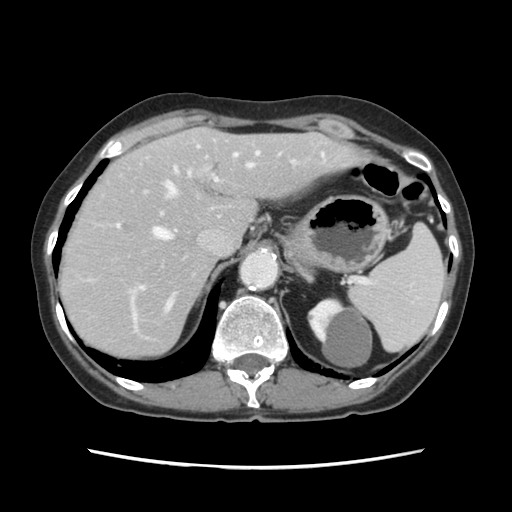
Contrast-enhanced abdominal CT, one axial slice; position 89 of 120 along the scan axis; intravenous contrast given; soft-tissue window (W 400 / L 40 HU); 512 × 512 image matrix, field of view 330 × 330 mm. Female patient, age 70 years. From the clinical record (not read from this slice): diagnosis: colorectal cancer liver metastases, imaged before liver resection; multiple liver metastases: no; largest metastasis: 2.5 cm; disease in both lobes: no.
Annotated regions visible in this slice (expert manual segmentation):
- hepatic veins: bounding box <153,153,253,313> (left, top, right, bottom; pixels)
- liver: <61,129,353,357>
- planned liver remnant (the part of the liver to remain after resection): <120,129,352,289>
- portal vein (with intrahepatic branches): <116,146,295,323>
- liver metastasis: <123,226,130,233>